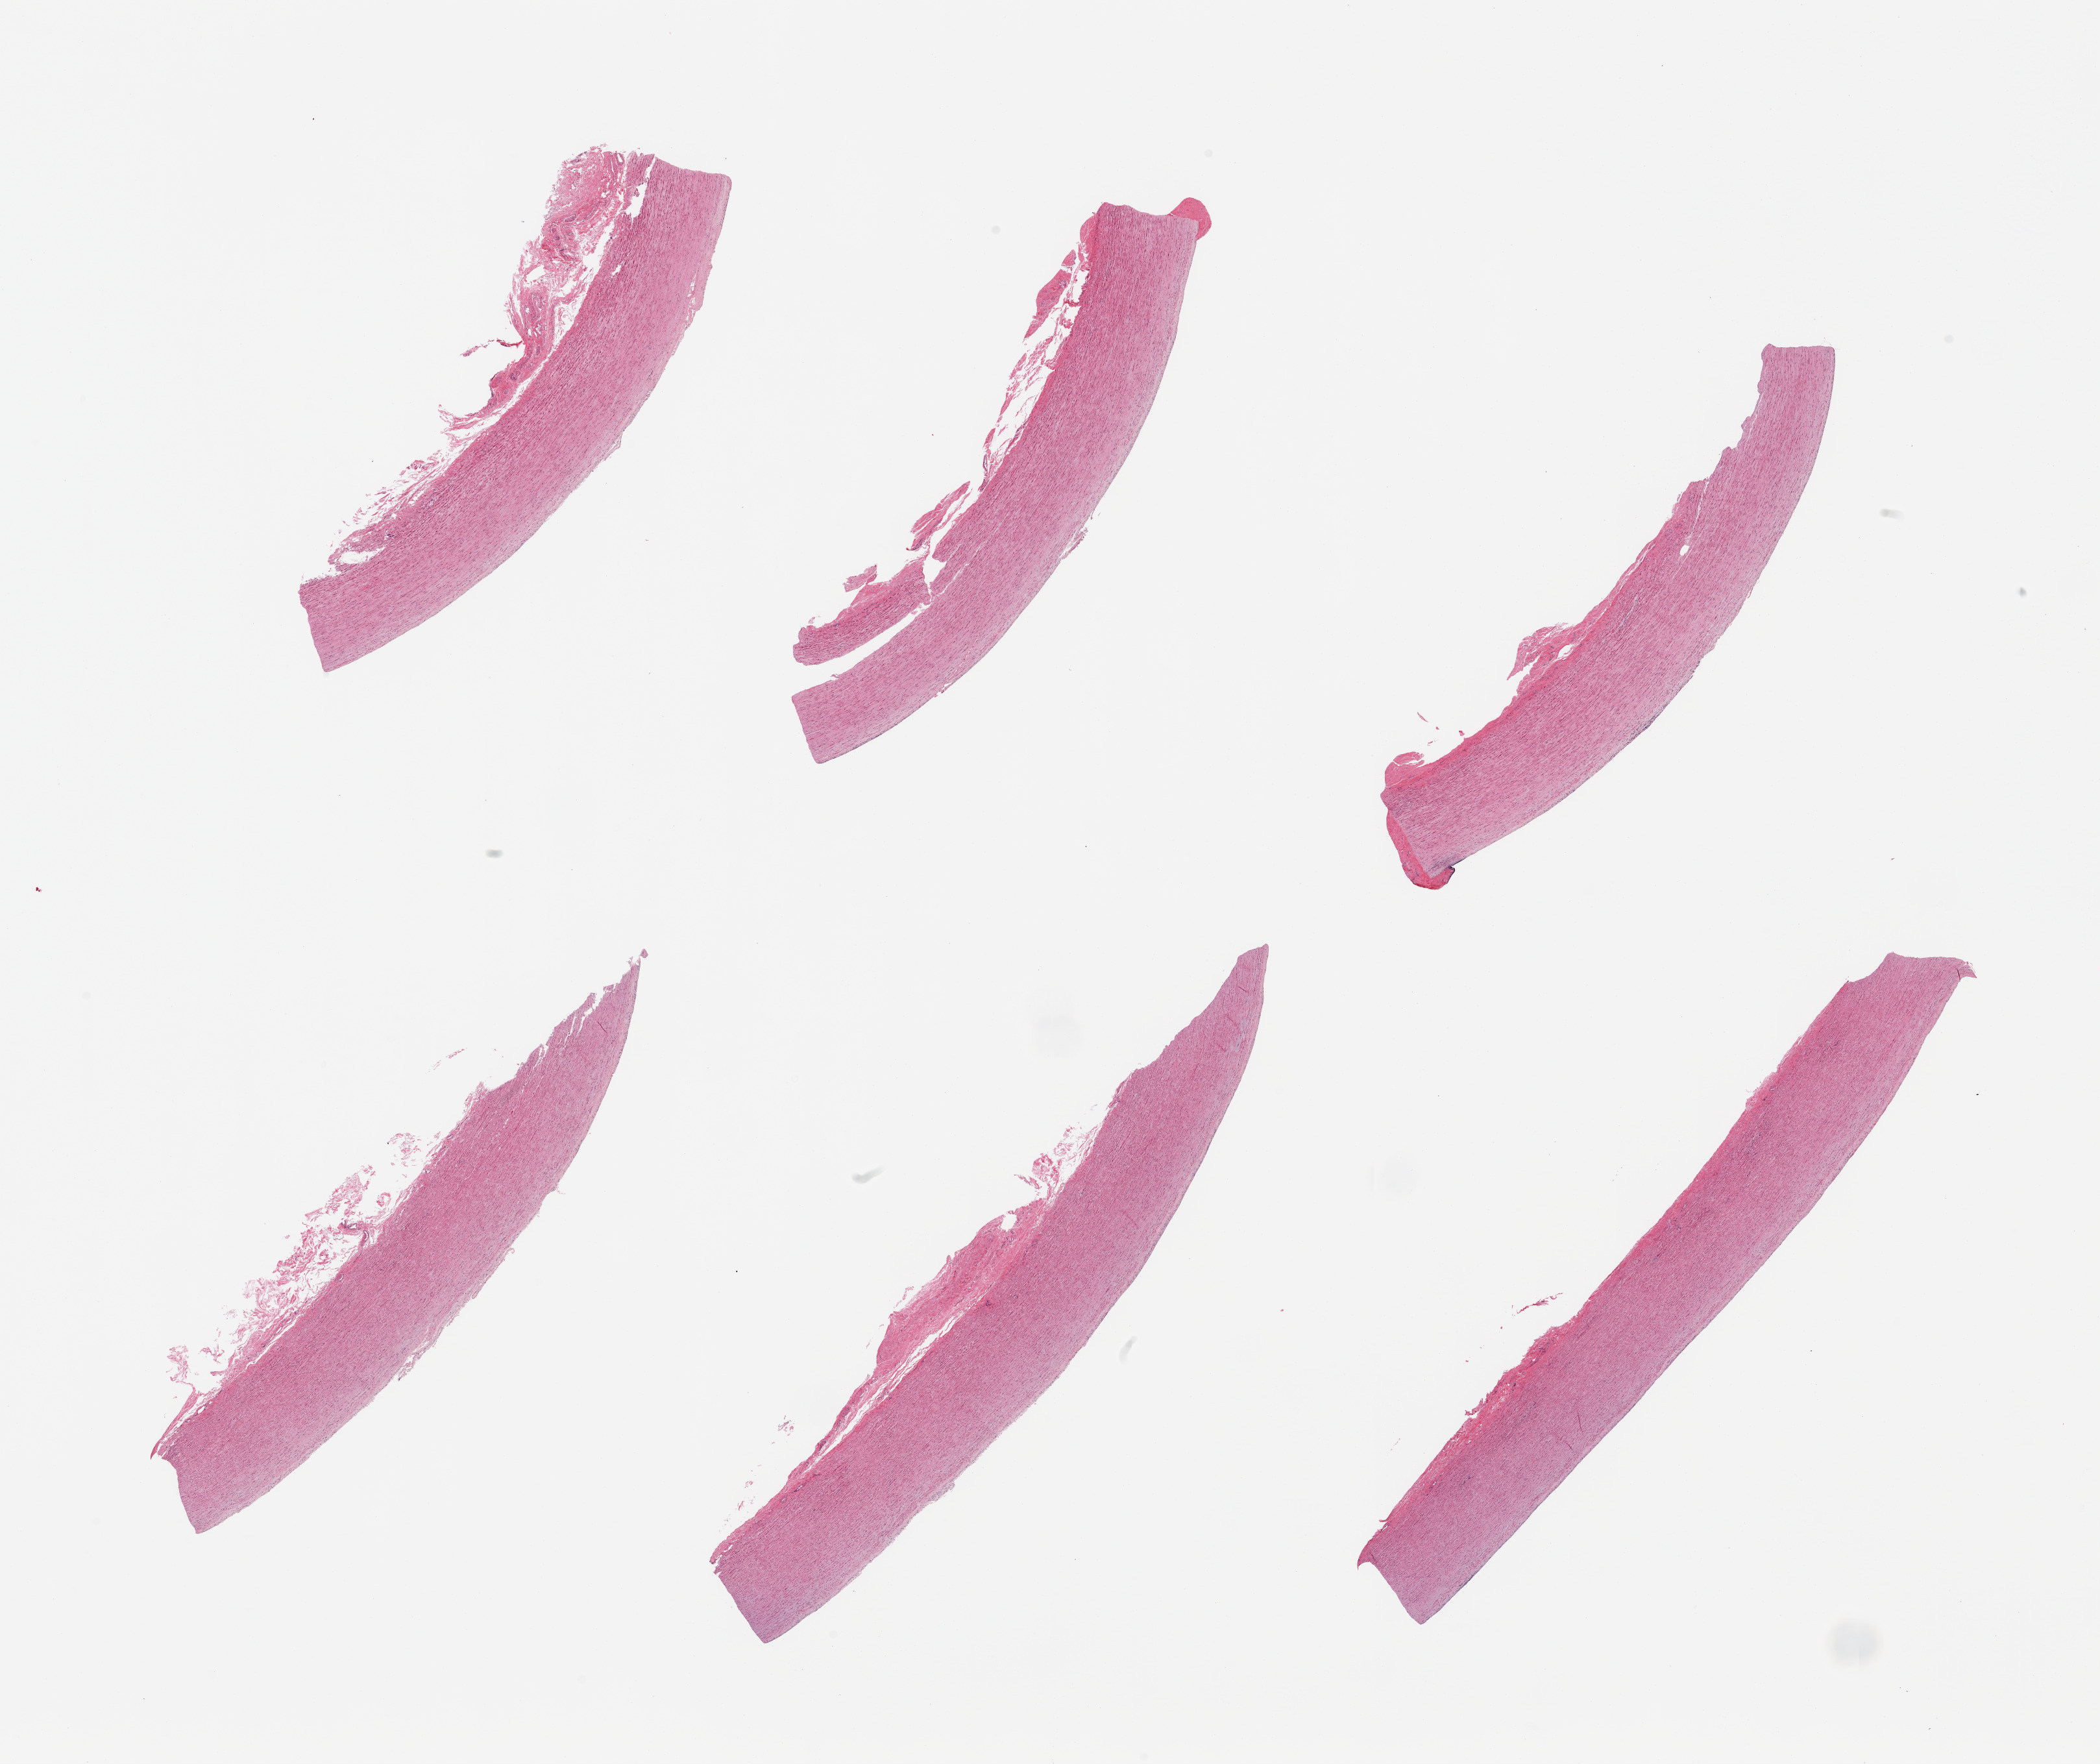
Digitized hematoxylin and eosin (H&E)-stained section — low-resolution overview of the scanned area, about 25.6 x 21.5 mm, PAXgene-fixed, paraffin-embedded tissue, section of aorta (target tissue), donor tissue sample.
• review note (as recorded): 6 pieces, no atherosis